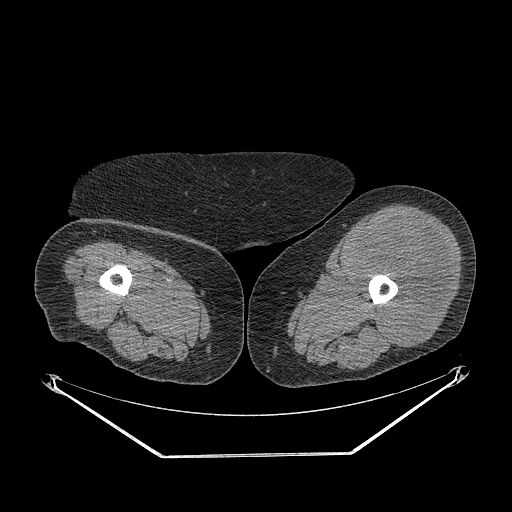
CT of an extremity soft-tissue mass (from a PET/CT study), one axial slice; position 231 of 267 along the scan axis; reconstruction kernel STANDARD; 140 kVp; soft-tissue window (W 400 / L 40 HU); 3.75 mm slice thickness; 512 × 512 image matrix, field of view 500 × 500 mm. Female patient. From the clinical record (not read from this slice): histological type: undifferentiated – high grade; grade: high; site of the primary tumour: left thigh.
Annotated regions visible in this slice (expert contour drawn on MRI and transferred to this co-registered scan by the dataset authors):
- gross tumour volume including surrounding oedema: bounding box <354,215,451,346> (left, top, right, bottom; pixels)
- gross tumour volume (mass): <354,215,451,346>